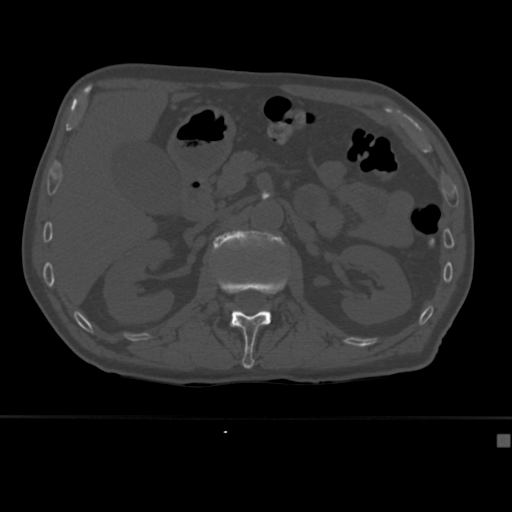
CT including the spine, one axial slice. Position 164 of 430 along the scan axis. Reconstruction kernel Br40s. Bone window (W 1800 / L 400 HU). 512 × 512 image matrix, field of view 337 × 337 mm. Patient: male, 64 years. Case-level facts recorded for this patient, not image findings: primary cancer: uterus.
Outlined on this slice (semi-automatic segmentation, software-assisted and operator-edited):
- L1 vertebra: bounding box (x1, y1, x2, y2) in pixels: (216, 251, 288, 369)
- L2 vertebra: (213, 230, 286, 283)